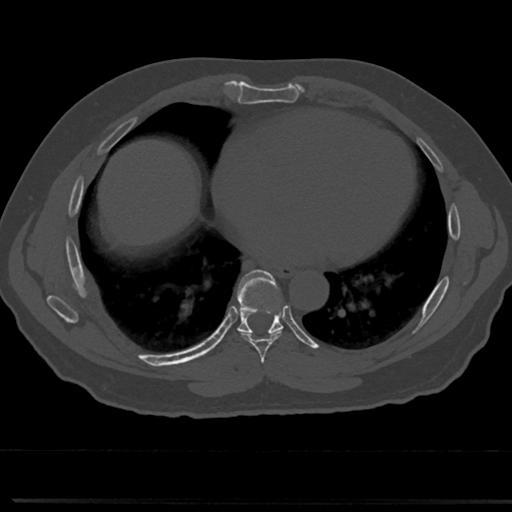
CT including the spine, one axial slice; position 381 of 817 along the scan axis; 120 kVp; bone window (W 1800 / L 400 HU); 0.5 mm slice thickness; 512 × 512 image matrix. Male patient, age 61 years. From the clinical record (not read from this slice): primary cancer: prostate.
Structures marked on this image (semi-automatically segmented with operator editing):
- T6 vertebra: bounding box [x1, y1, x2, y2] px = [260, 368, 267, 376]
- T7 vertebra: [230, 273, 304, 353]